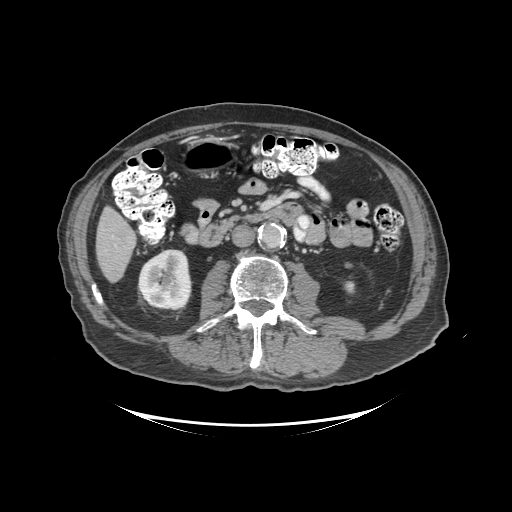
Contrast-enhanced abdominal CT (liver protocol), one axial slice; slice 30 of 99 in the series (ordered by position); 140 kVp; soft-tissue window (W 400 / L 40 HU); 512 × 512 image matrix, field of view 460 × 460 mm. From the clinical record (not read from this slice): diagnosis: hepatocellular carcinoma (patient treated with transarterial chemoembolisation; whether this scan precedes or follows treatment is not stated here); TNM stage (as recorded): Stage-I; Child-Pugh class: A; tumour differentiation: moderately differentiated; tumour nodularity: uninodular.
Structures marked on this image (semi-automatic segmentation, software-assisted and operator-edited):
- liver parenchyma outside the tumour (the mass and vessels are separate outlines, so this box may not span the whole liver): box from (x=96, y=206) to (x=136, y=282) px